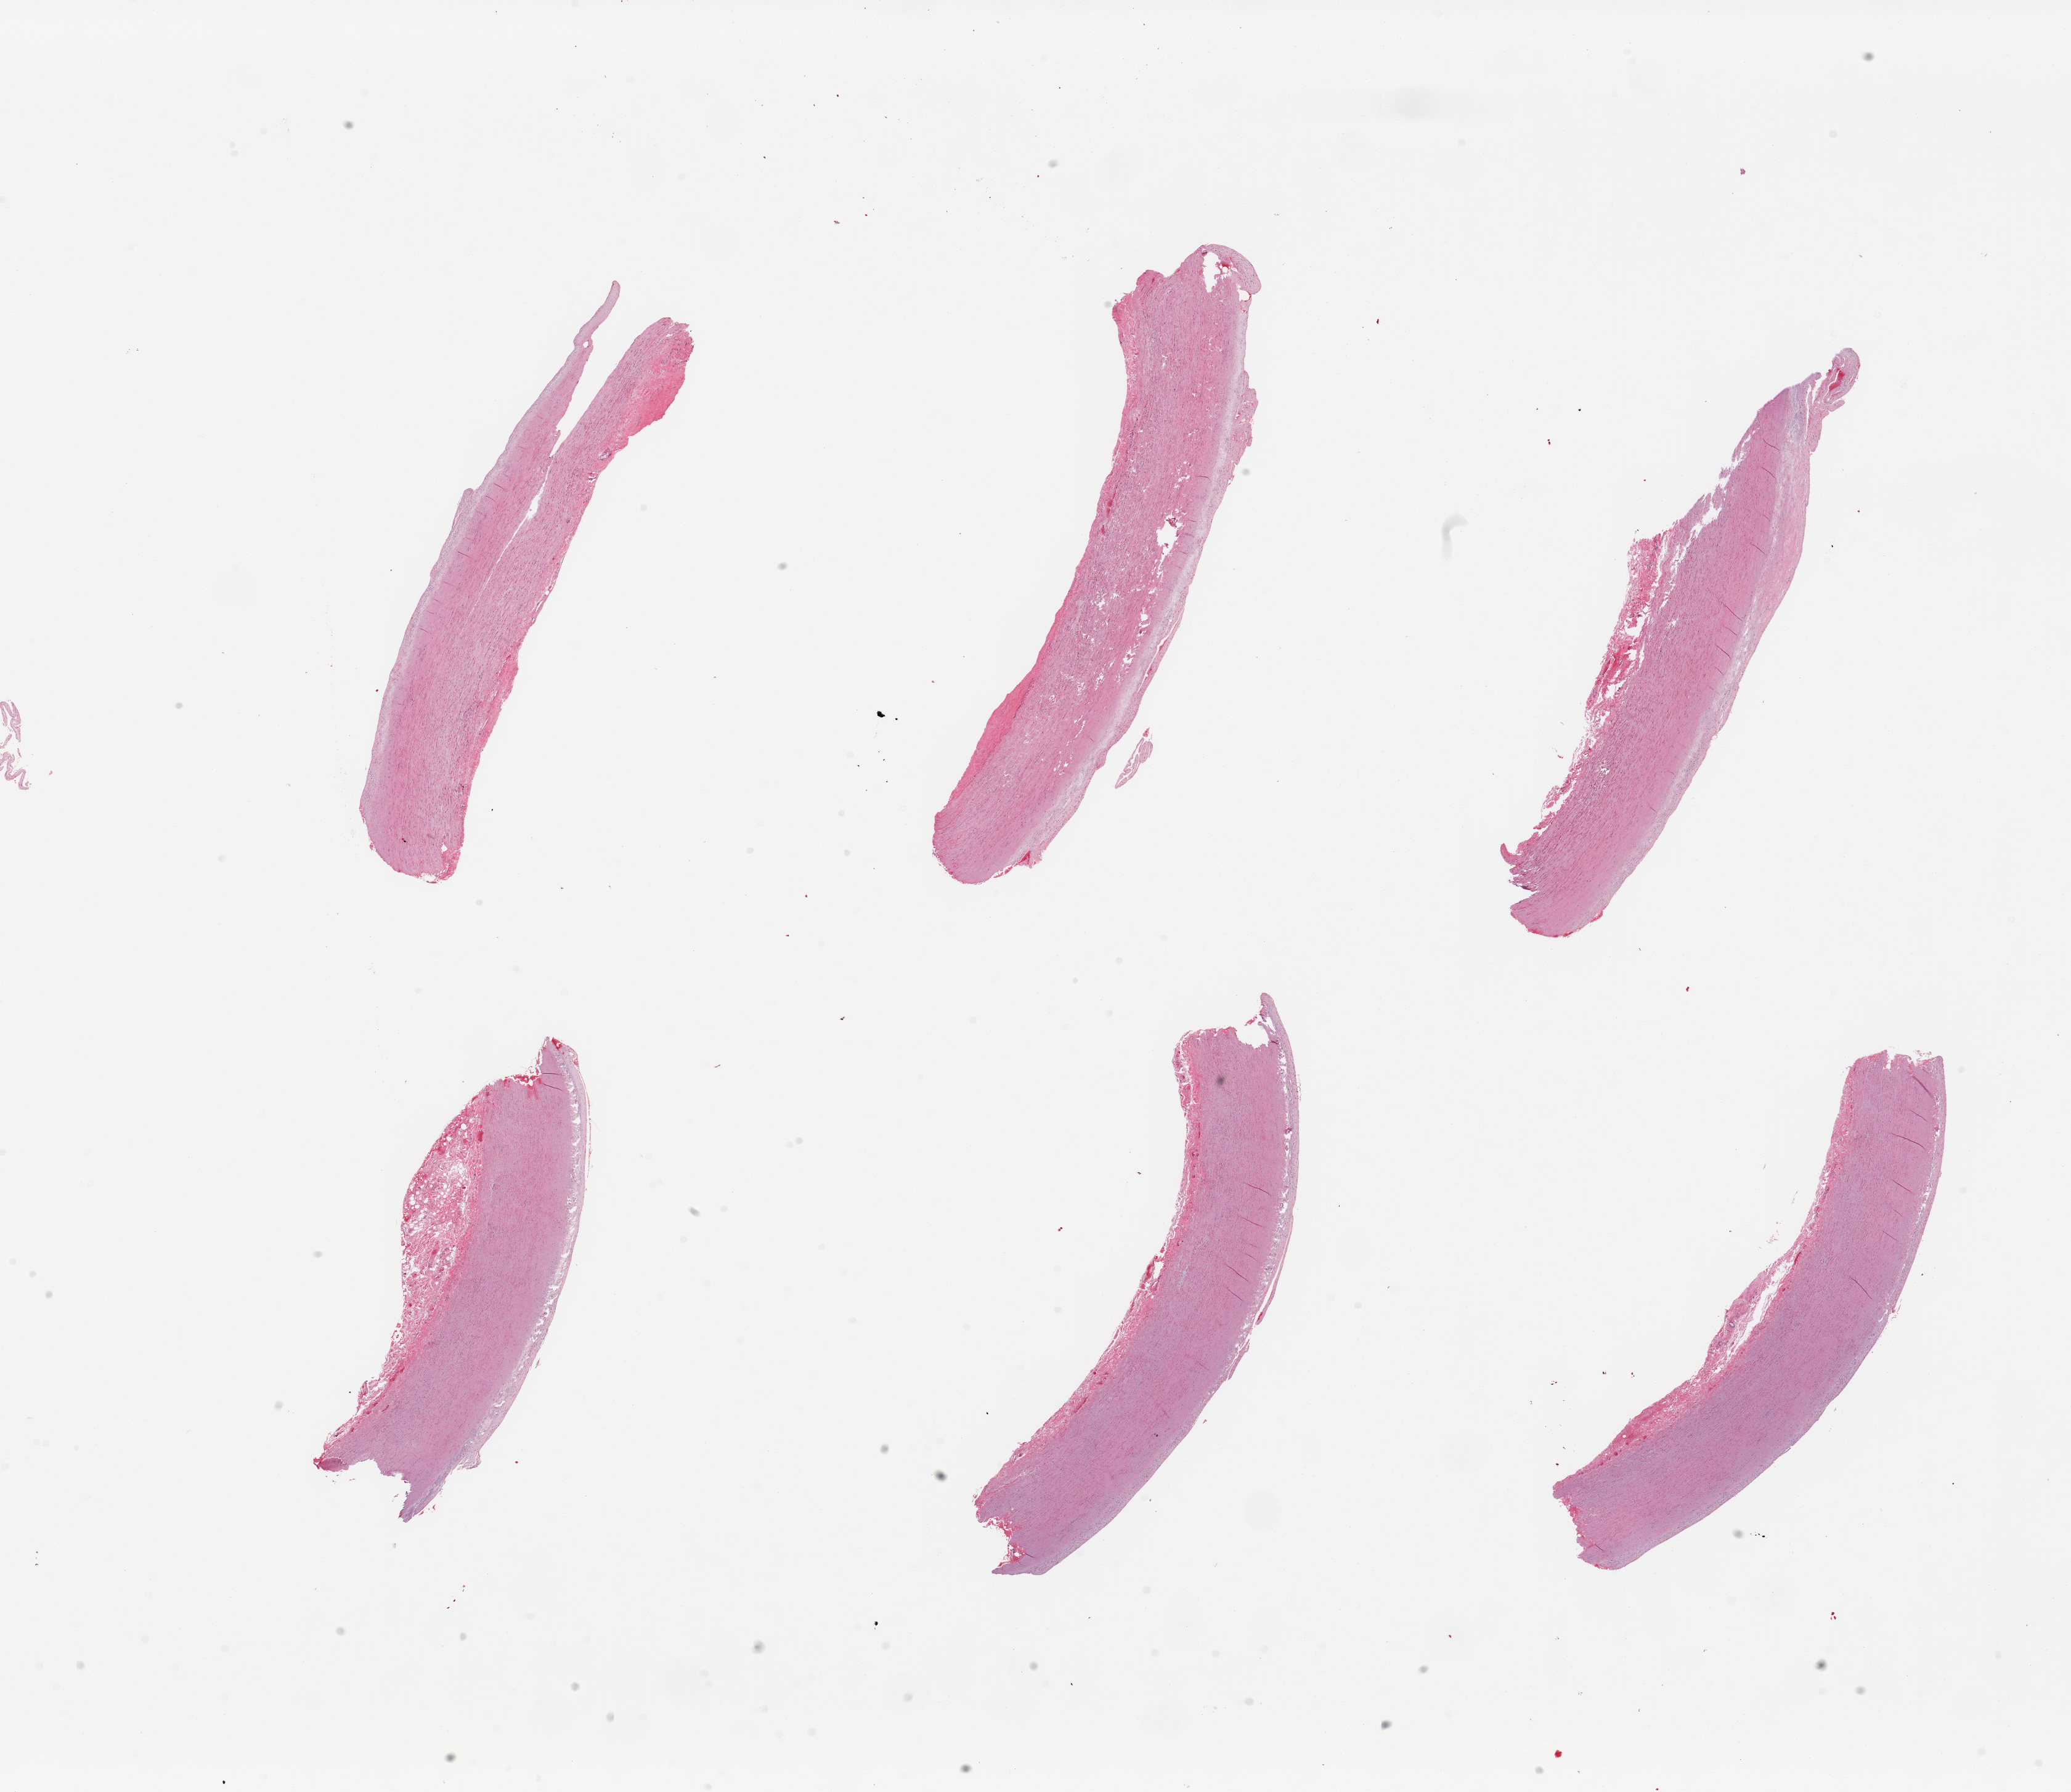
Whole-slide image, H&E stain, a low-resolution overview of the entire scanned area, about 26.6 x 23.0 mm. PAXgene-fixed paraffin-embedded (PFPE) section. Sampled site (target tissue): aorta. Donor tissue sample. Donor sex: male.
• review note (as recorded): 6 pieces; 5 well trimmed; flat plaques